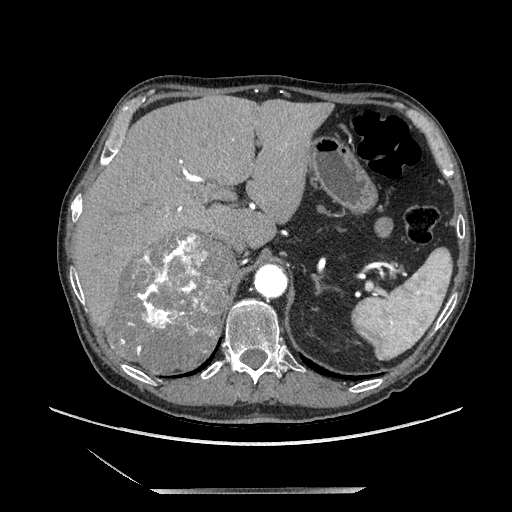
Contrast-enhanced abdominal CT, one axial slice; position 150 of 243 along the scan axis; soft-tissue window (W 400 / L 40 HU); 1.25 mm slice thickness; 512 × 512 image matrix, field of view 420 × 420 mm. Male patient. Case-level facts recorded for this patient, not image findings: diagnosis: adrenocortical carcinoma; tumour side: right adrenal; tumour size at pathology: 16 cm; Ki-67 index: 17 %; stage (as recorded): 3.
Annotated regions visible in this slice (semi-automatic segmentation, software-assisted and operator-edited):
- mass: bounding box <112,233,238,375> (left, top, right, bottom; pixels)